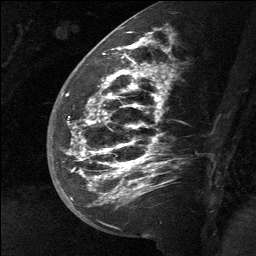
Breast MRI (dynamic contrast-enhanced), one sagittal slice. Position 28 of 64 along the scan axis. Dynamic contrast-enhanced study with each time point stored as its own series, time point 2 of 3 at this slice position (early post-contrast, ordered by acquisition time). 1.5 T. TE 4.8 ms, TR 27 ms. 256 × 256 image matrix. Patient: female, 39 years. From the clinical record (not read from this slice): setting: breast cancer imaged before/during neoadjuvant chemotherapy; receptor status: HER2-positive.
Outlined on this slice (semi-automatically segmented with operator editing):
- analysis volume of interest (the breast-tissue region the enhancement analysis was run in; not a lesion): box from (x=58, y=40) to (x=169, y=217) px
- tumour enhancement mask (voxels above the 90 % enhancement threshold inside the analysis volume of interest): (x=66, y=40)–(x=155, y=198)